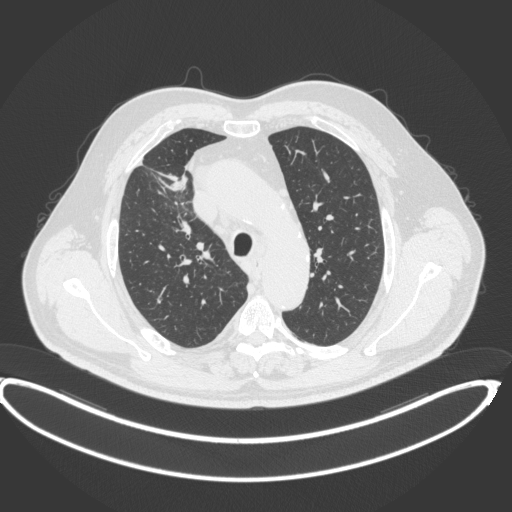
Chest CT, one axial slice; position 304 of 395 along the scan axis; reconstruction kernel B31f; 120 kVp; lung window (W 1500 / L -600 HU); 1 mm slice thickness; 512 × 512 image matrix. Male patient, age 62 years. From the clinical record (not read from this slice): clinical TNM (as recorded): T1c N3 M1c.
Structures marked on this image (bounding box drawn by a radiologist):
- lung tumour (recorded histology: adenocarcinoma): box from (x=167, y=174) to (x=188, y=192) px